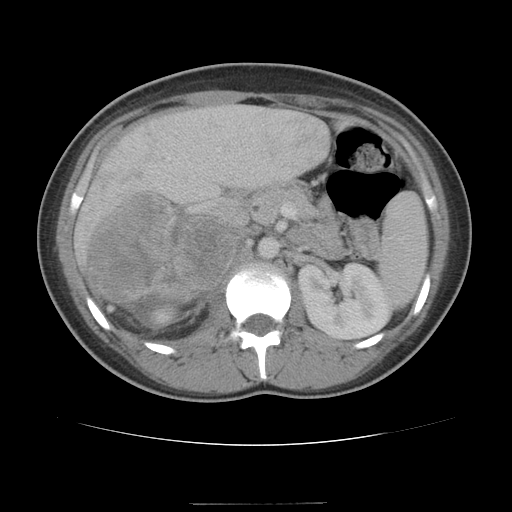
Contrast-enhanced abdominal CT, one axial slice; position 67 of 100 along the scan axis; 120 kVp; soft-tissue window (W 400 / L 40 HU); 5 mm slice thickness; 512 × 512 image matrix, field of view 360 × 360 mm. Patient: female, 21 years. Case-level facts recorded for this patient, not image findings: diagnosis: adrenocortical carcinoma; tumour side: right adrenal; tumour size at pathology: 15.5 cm; Ki-67 index: 26 %; stage (as recorded): 3.
Annotated regions visible in this slice (semi-automatically segmented with operator editing):
- mass: bounding box (x1, y1, x2, y2) in pixels: (90, 194, 232, 302)